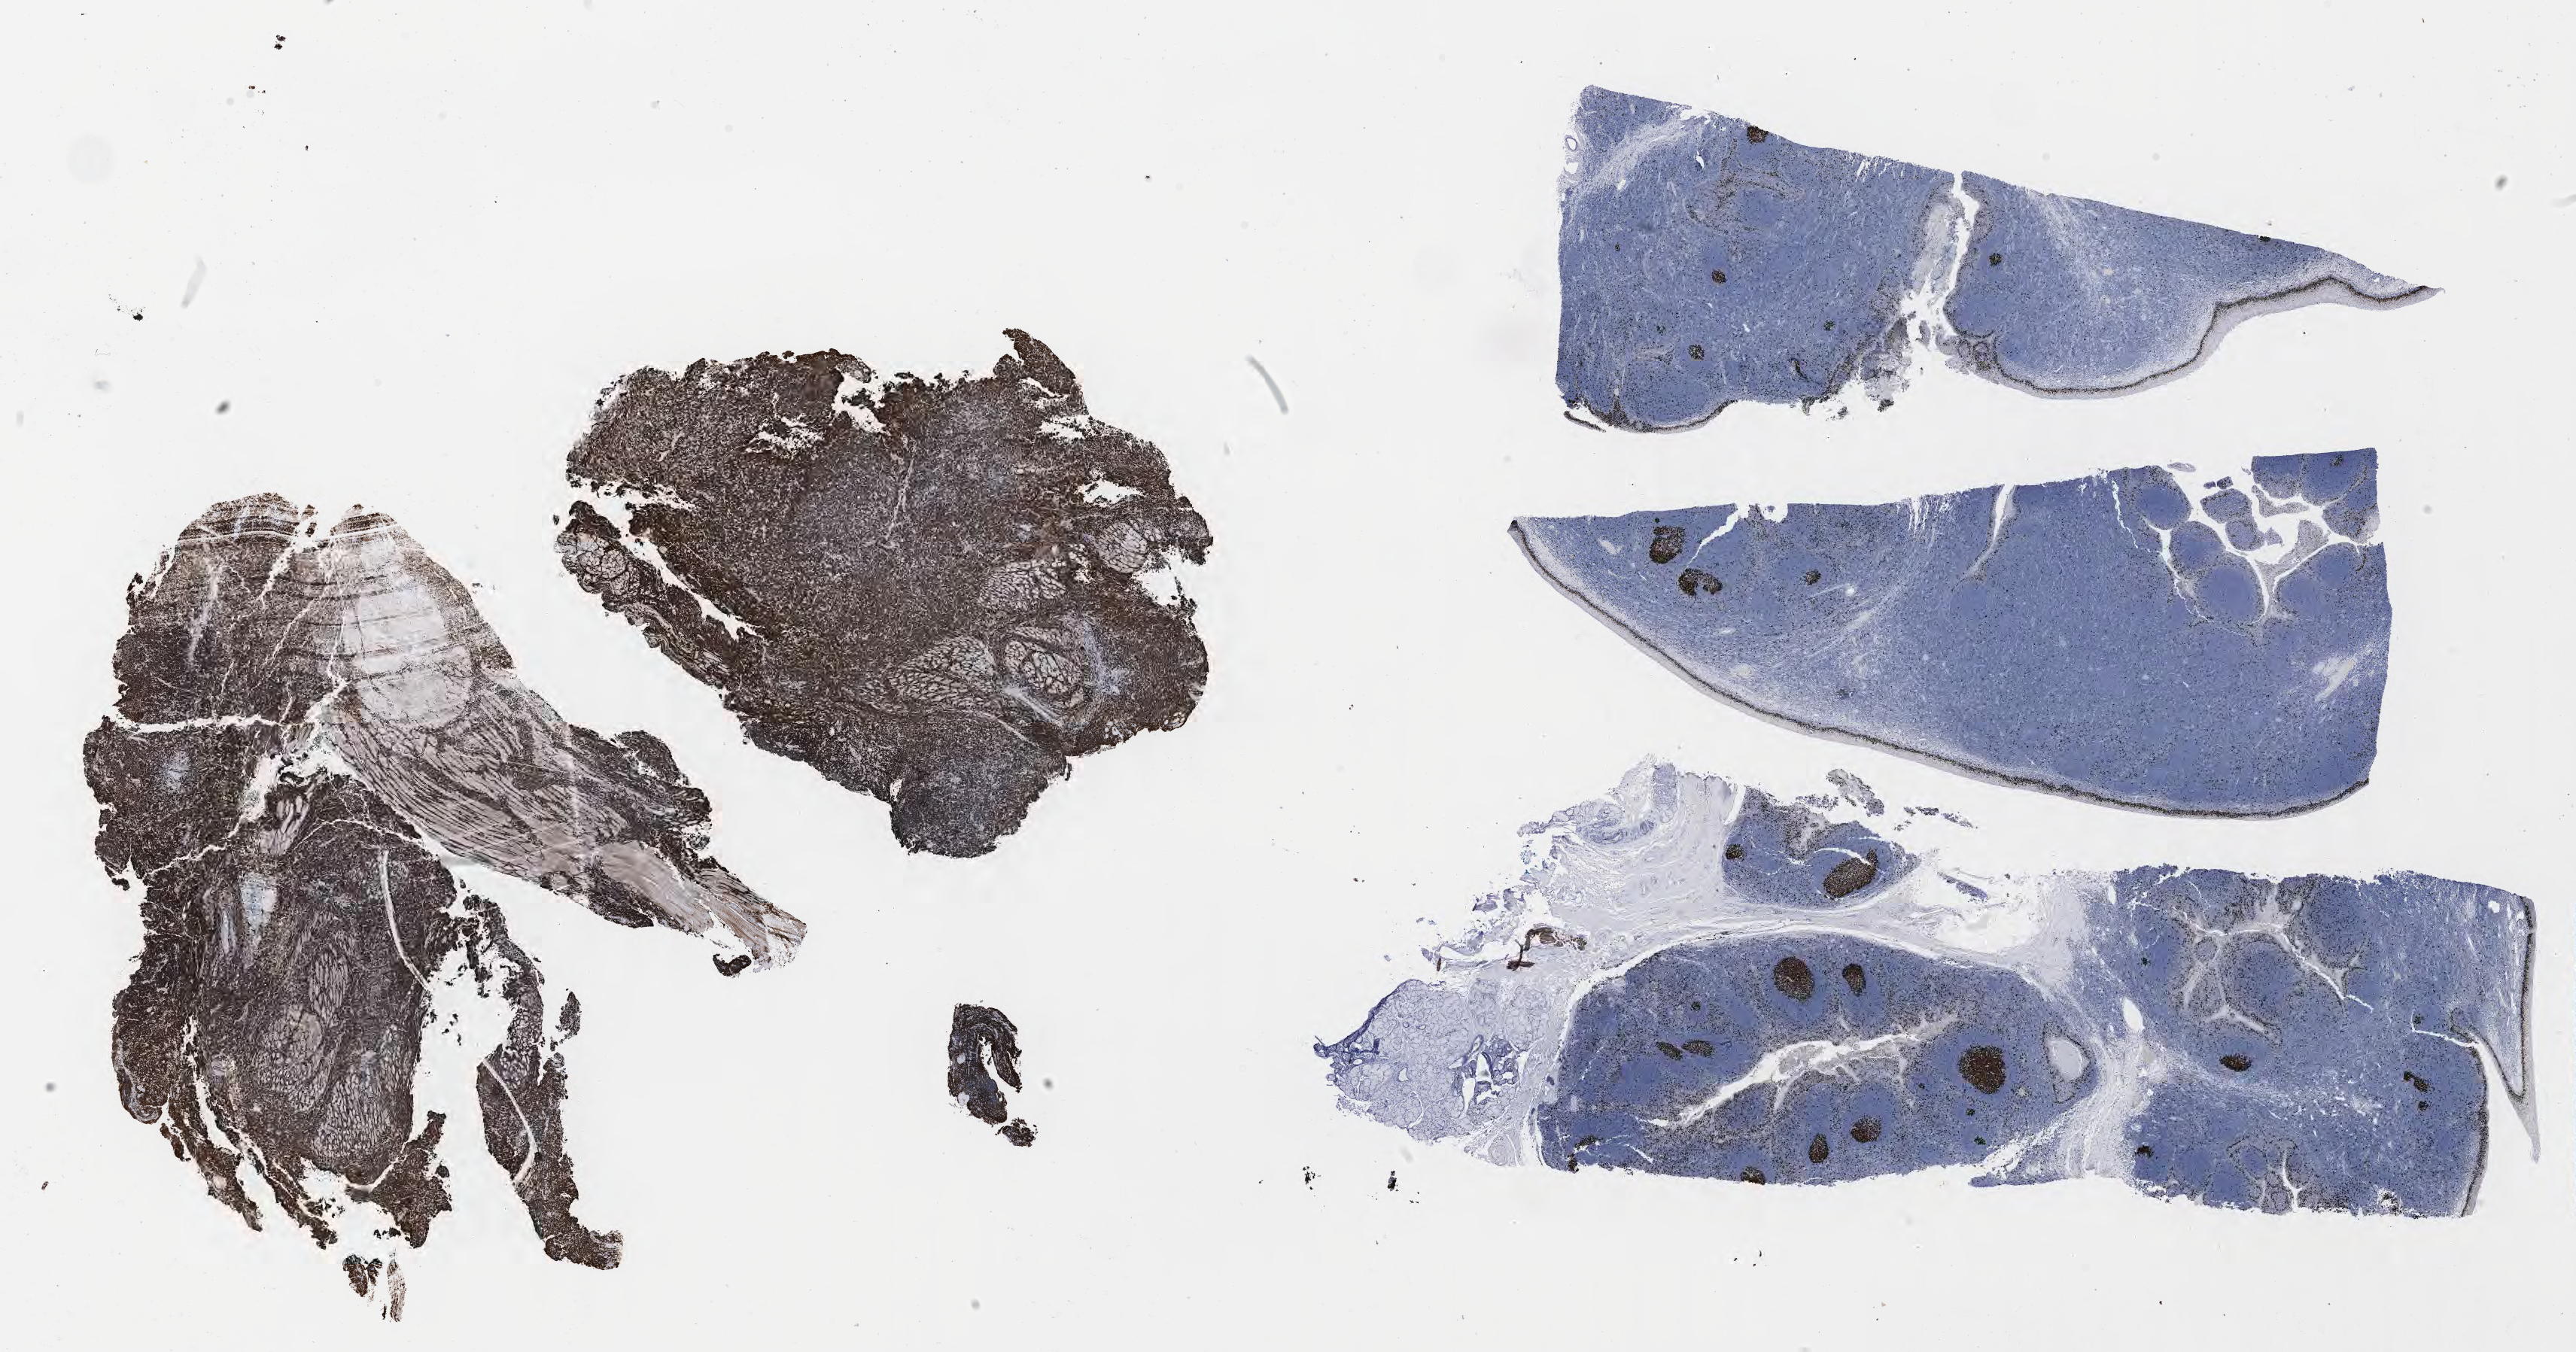
Whole-slide image, immunohistochemical stain for Ki-67 — a low-resolution overview of the entire scanned area, about 27.7 x 14.5 mm; specimen: tumor tissue; anatomic site: pelvis. Male patient; age at initial diagnosis 7 years.
Diagnosis: Diffuse large B-cell lymphoma, NOS.